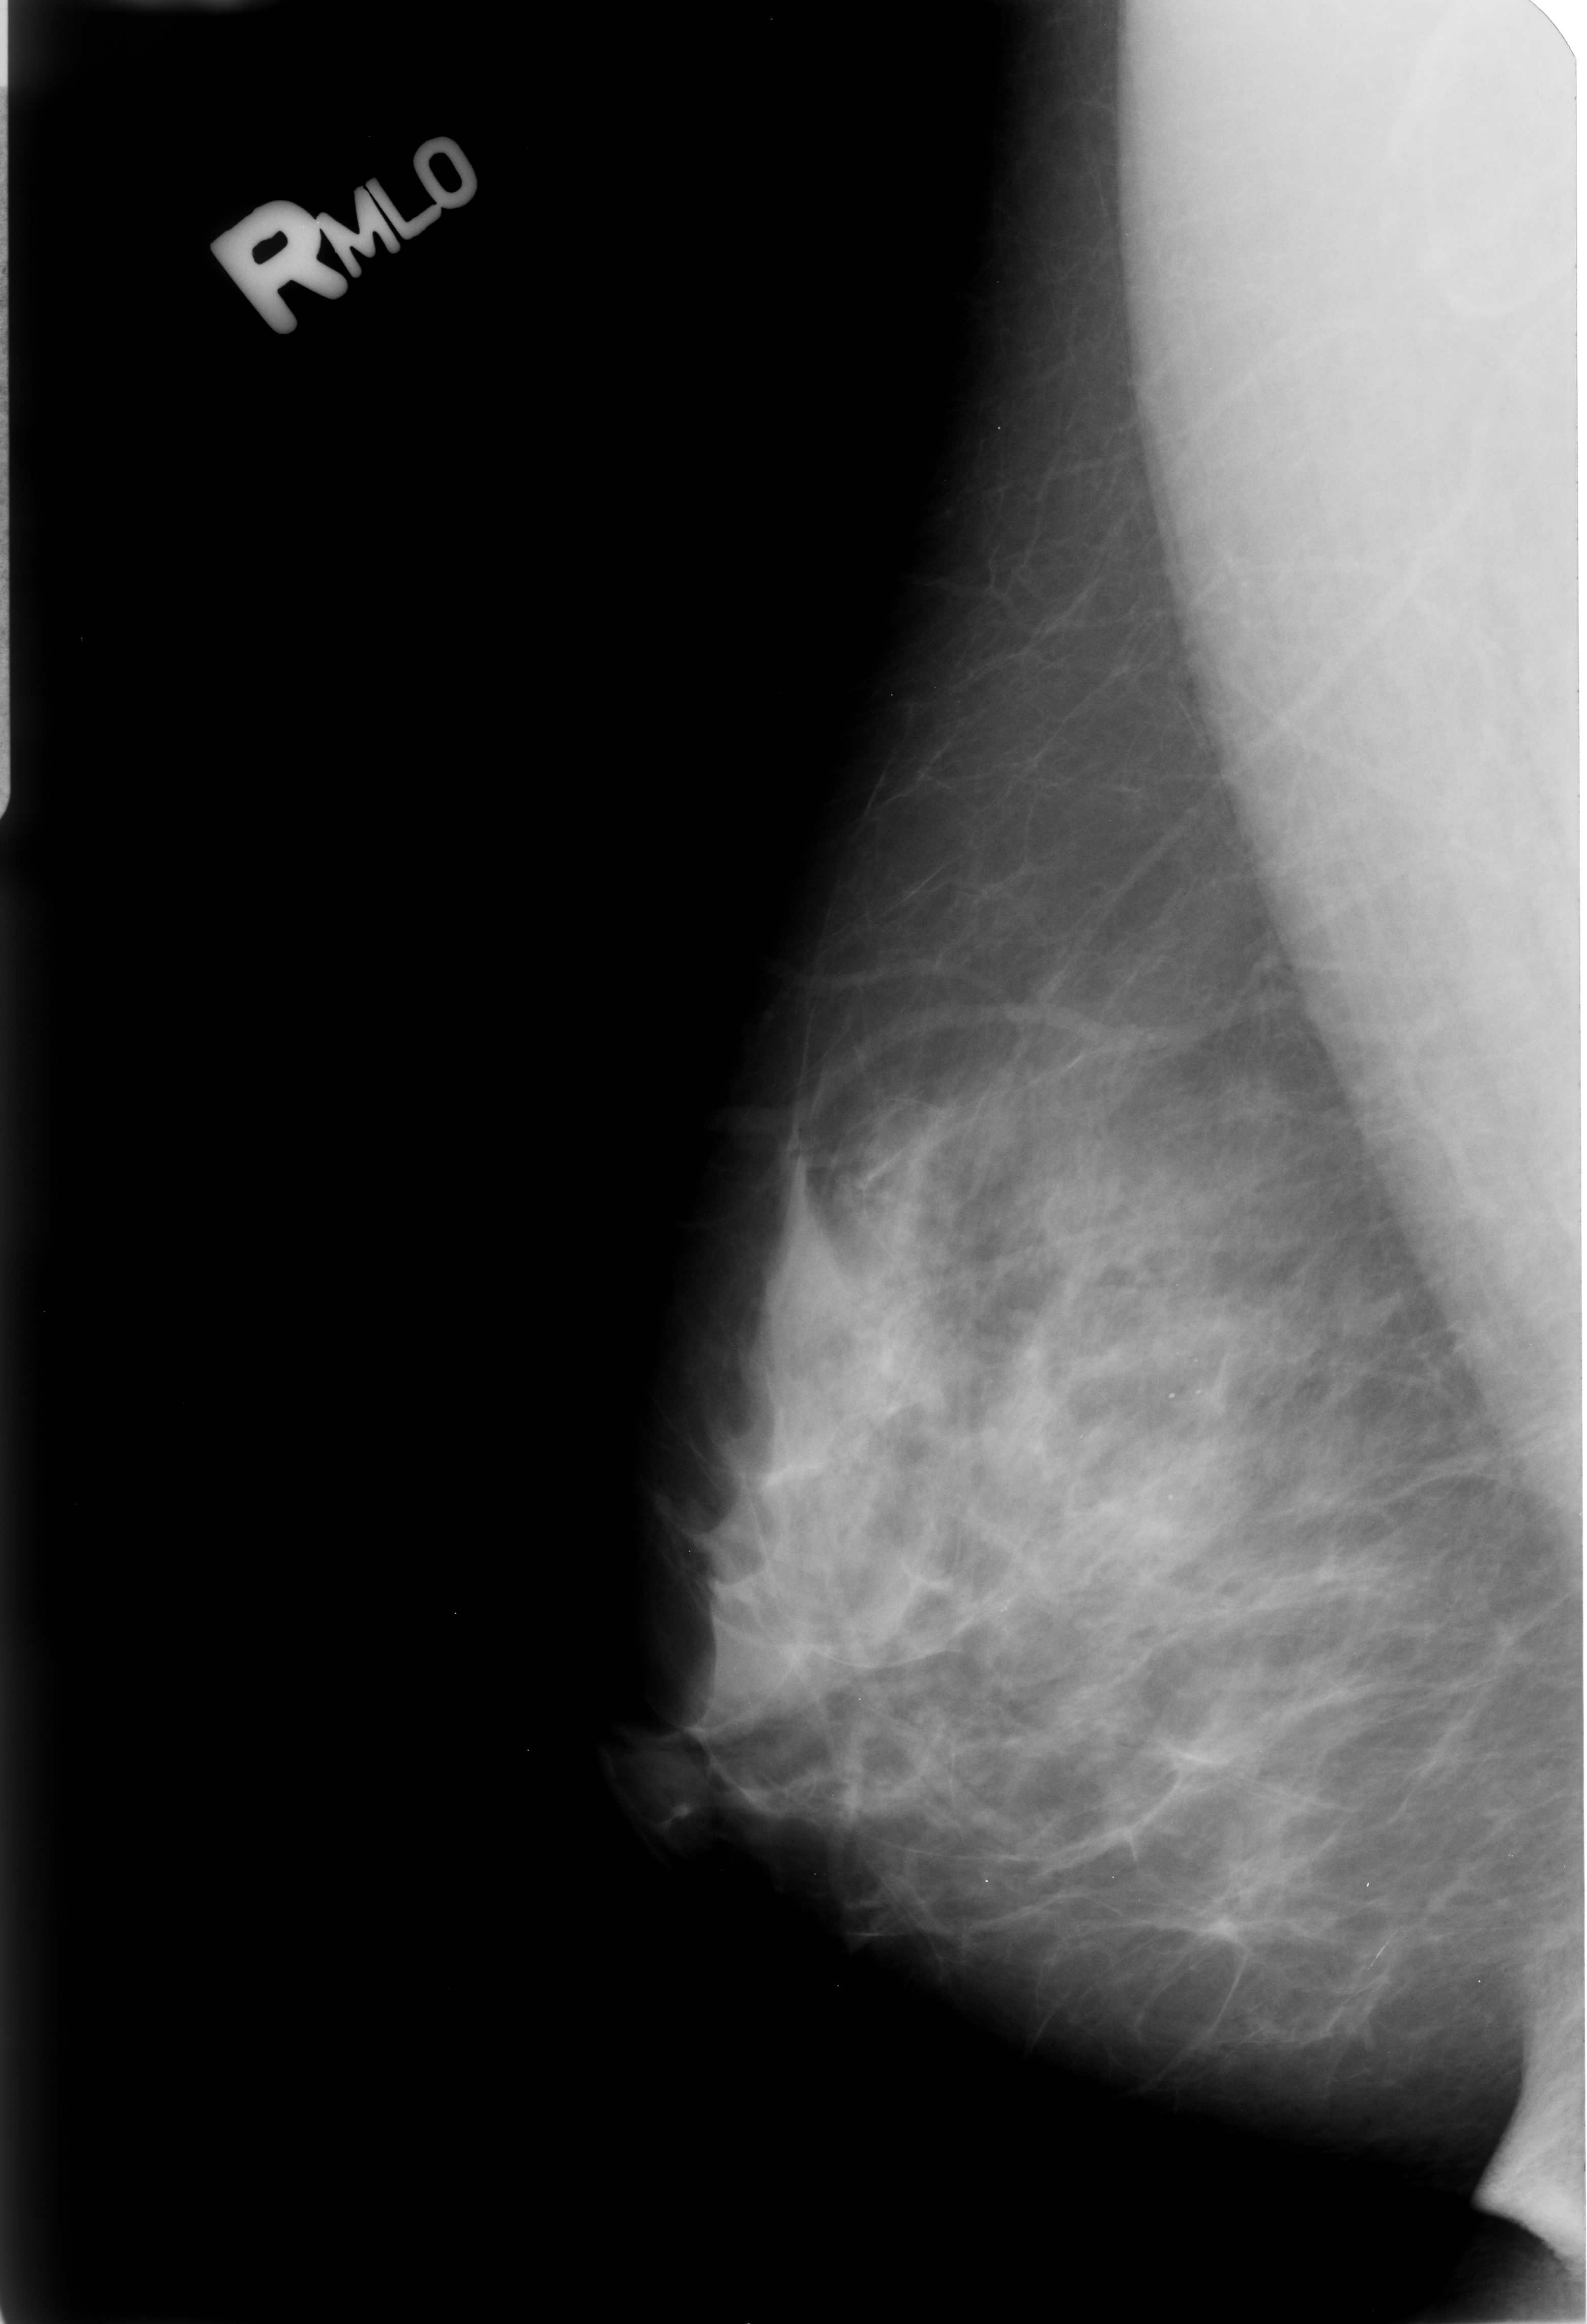
Scanned film-screen mammogram, right breast, MLO view.
Abnormality record for this image: Finding 1 of 2: calcifications, morphology punctate / round and regular, distribution regional; BI-RADS assessment category 2; subtlety rating 3 on a 1 (subtle) to 5 (obvious) scale; benign; no additional work-up was recommended (benign without callback). Finding 2 of 2: calcifications, morphology punctate / round and regular, distribution regional; BI-RADS assessment category 2; subtlety rating 3 on a 1 (subtle) to 5 (obvious) scale; benign; no additional work-up was recommended (benign without callback).